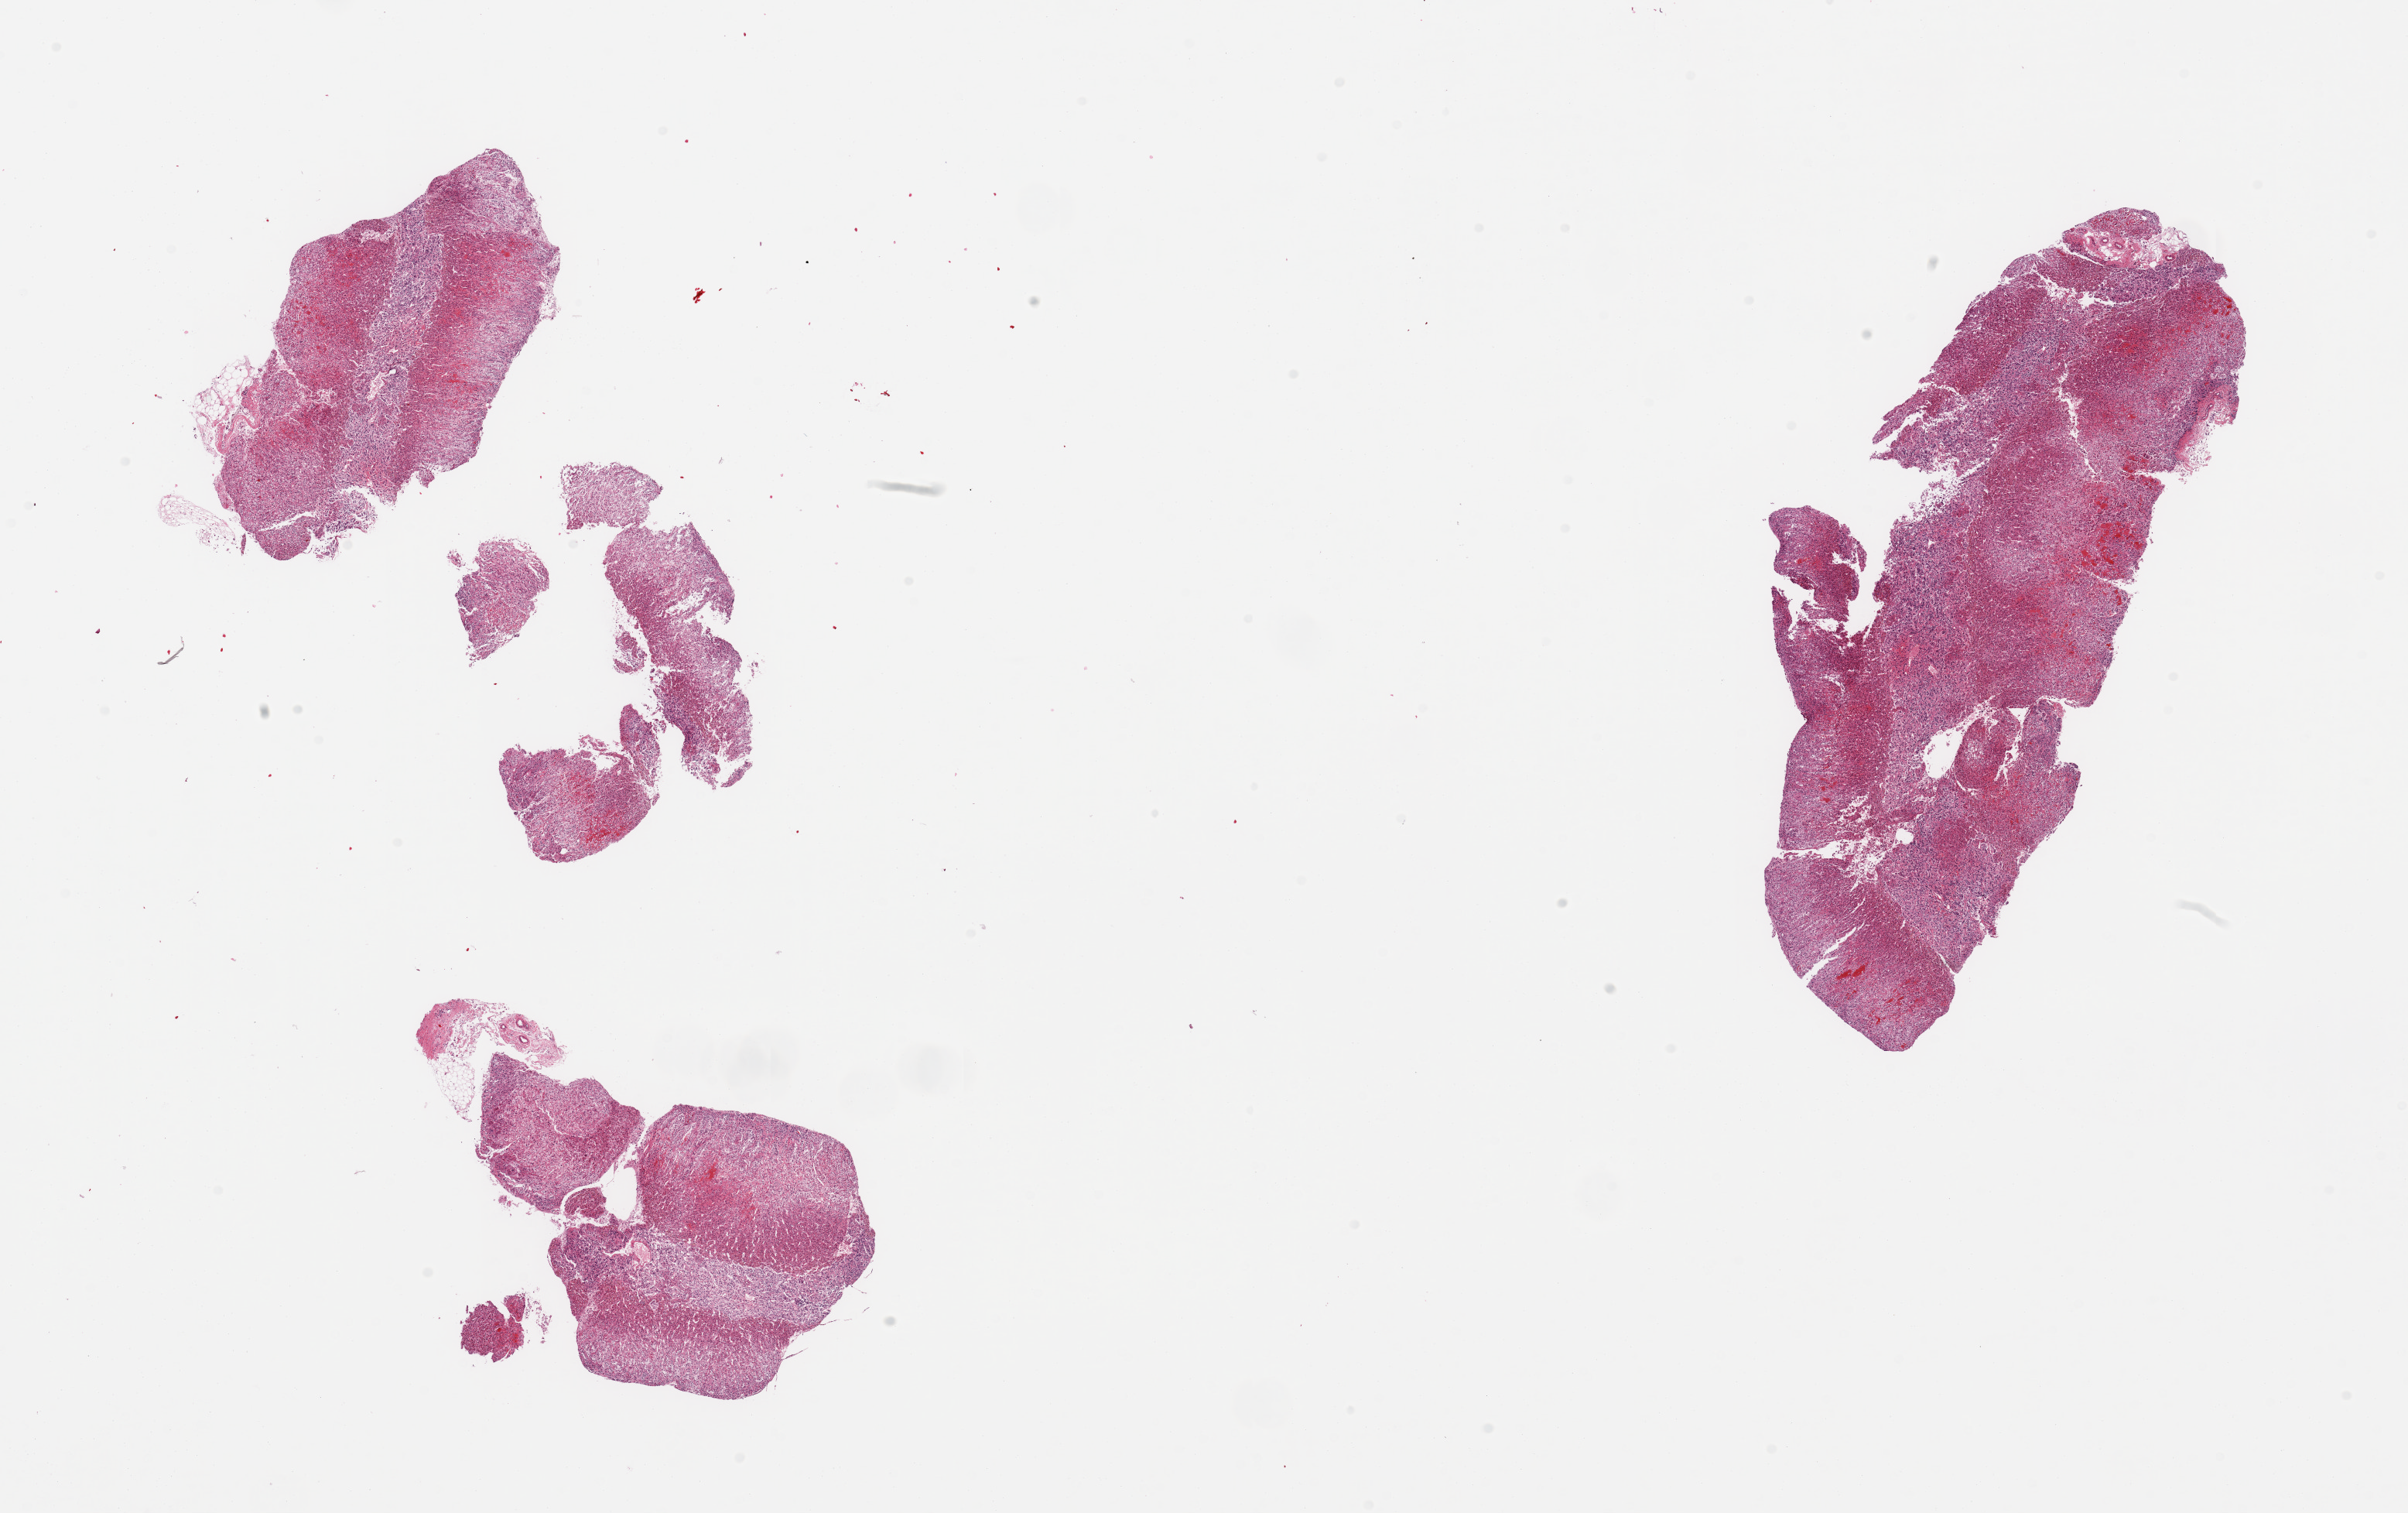
Digitized haematoxylin and eosin-stained section — shown as a low-resolution overview of the whole scanned area (about 24.6 x 15.5 mm), PAXgene-fixed paraffin-embedded (PFPE) section, sampled site (target tissue): adrenal gland, donor tissue sample. Donor sex: male.
Pathologist's review note for this sample: 2 pieces (fragmented); adrenal cortex and medulla.